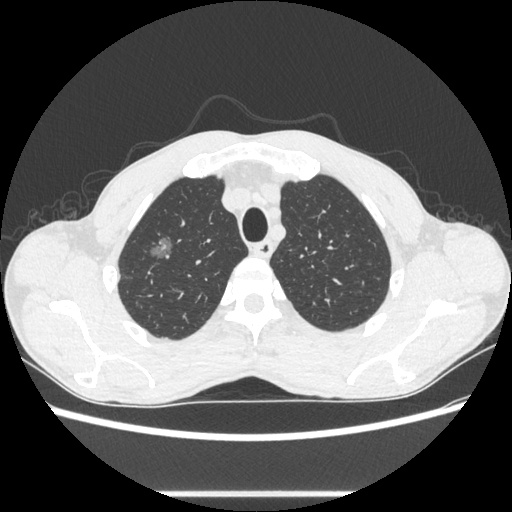
Chest CT, one axial slice. Position 493 of 600 along the scan axis. Reconstruction kernel STANDARD. 100 kVp. Lung window (W 1500 / L -600 HU). 0.62 mm slice thickness. 512 × 512 image matrix, field of view 357 × 357 mm. Male patient, age 54 years. Case-level facts recorded for this patient, not image findings: clinical TNM (as recorded): T1a N0 M0.
Structures marked on this image (rectangle marked by the reading radiologist):
- lung tumour (recorded histology: adenocarcinoma): box from (x=142, y=226) to (x=178, y=268) px